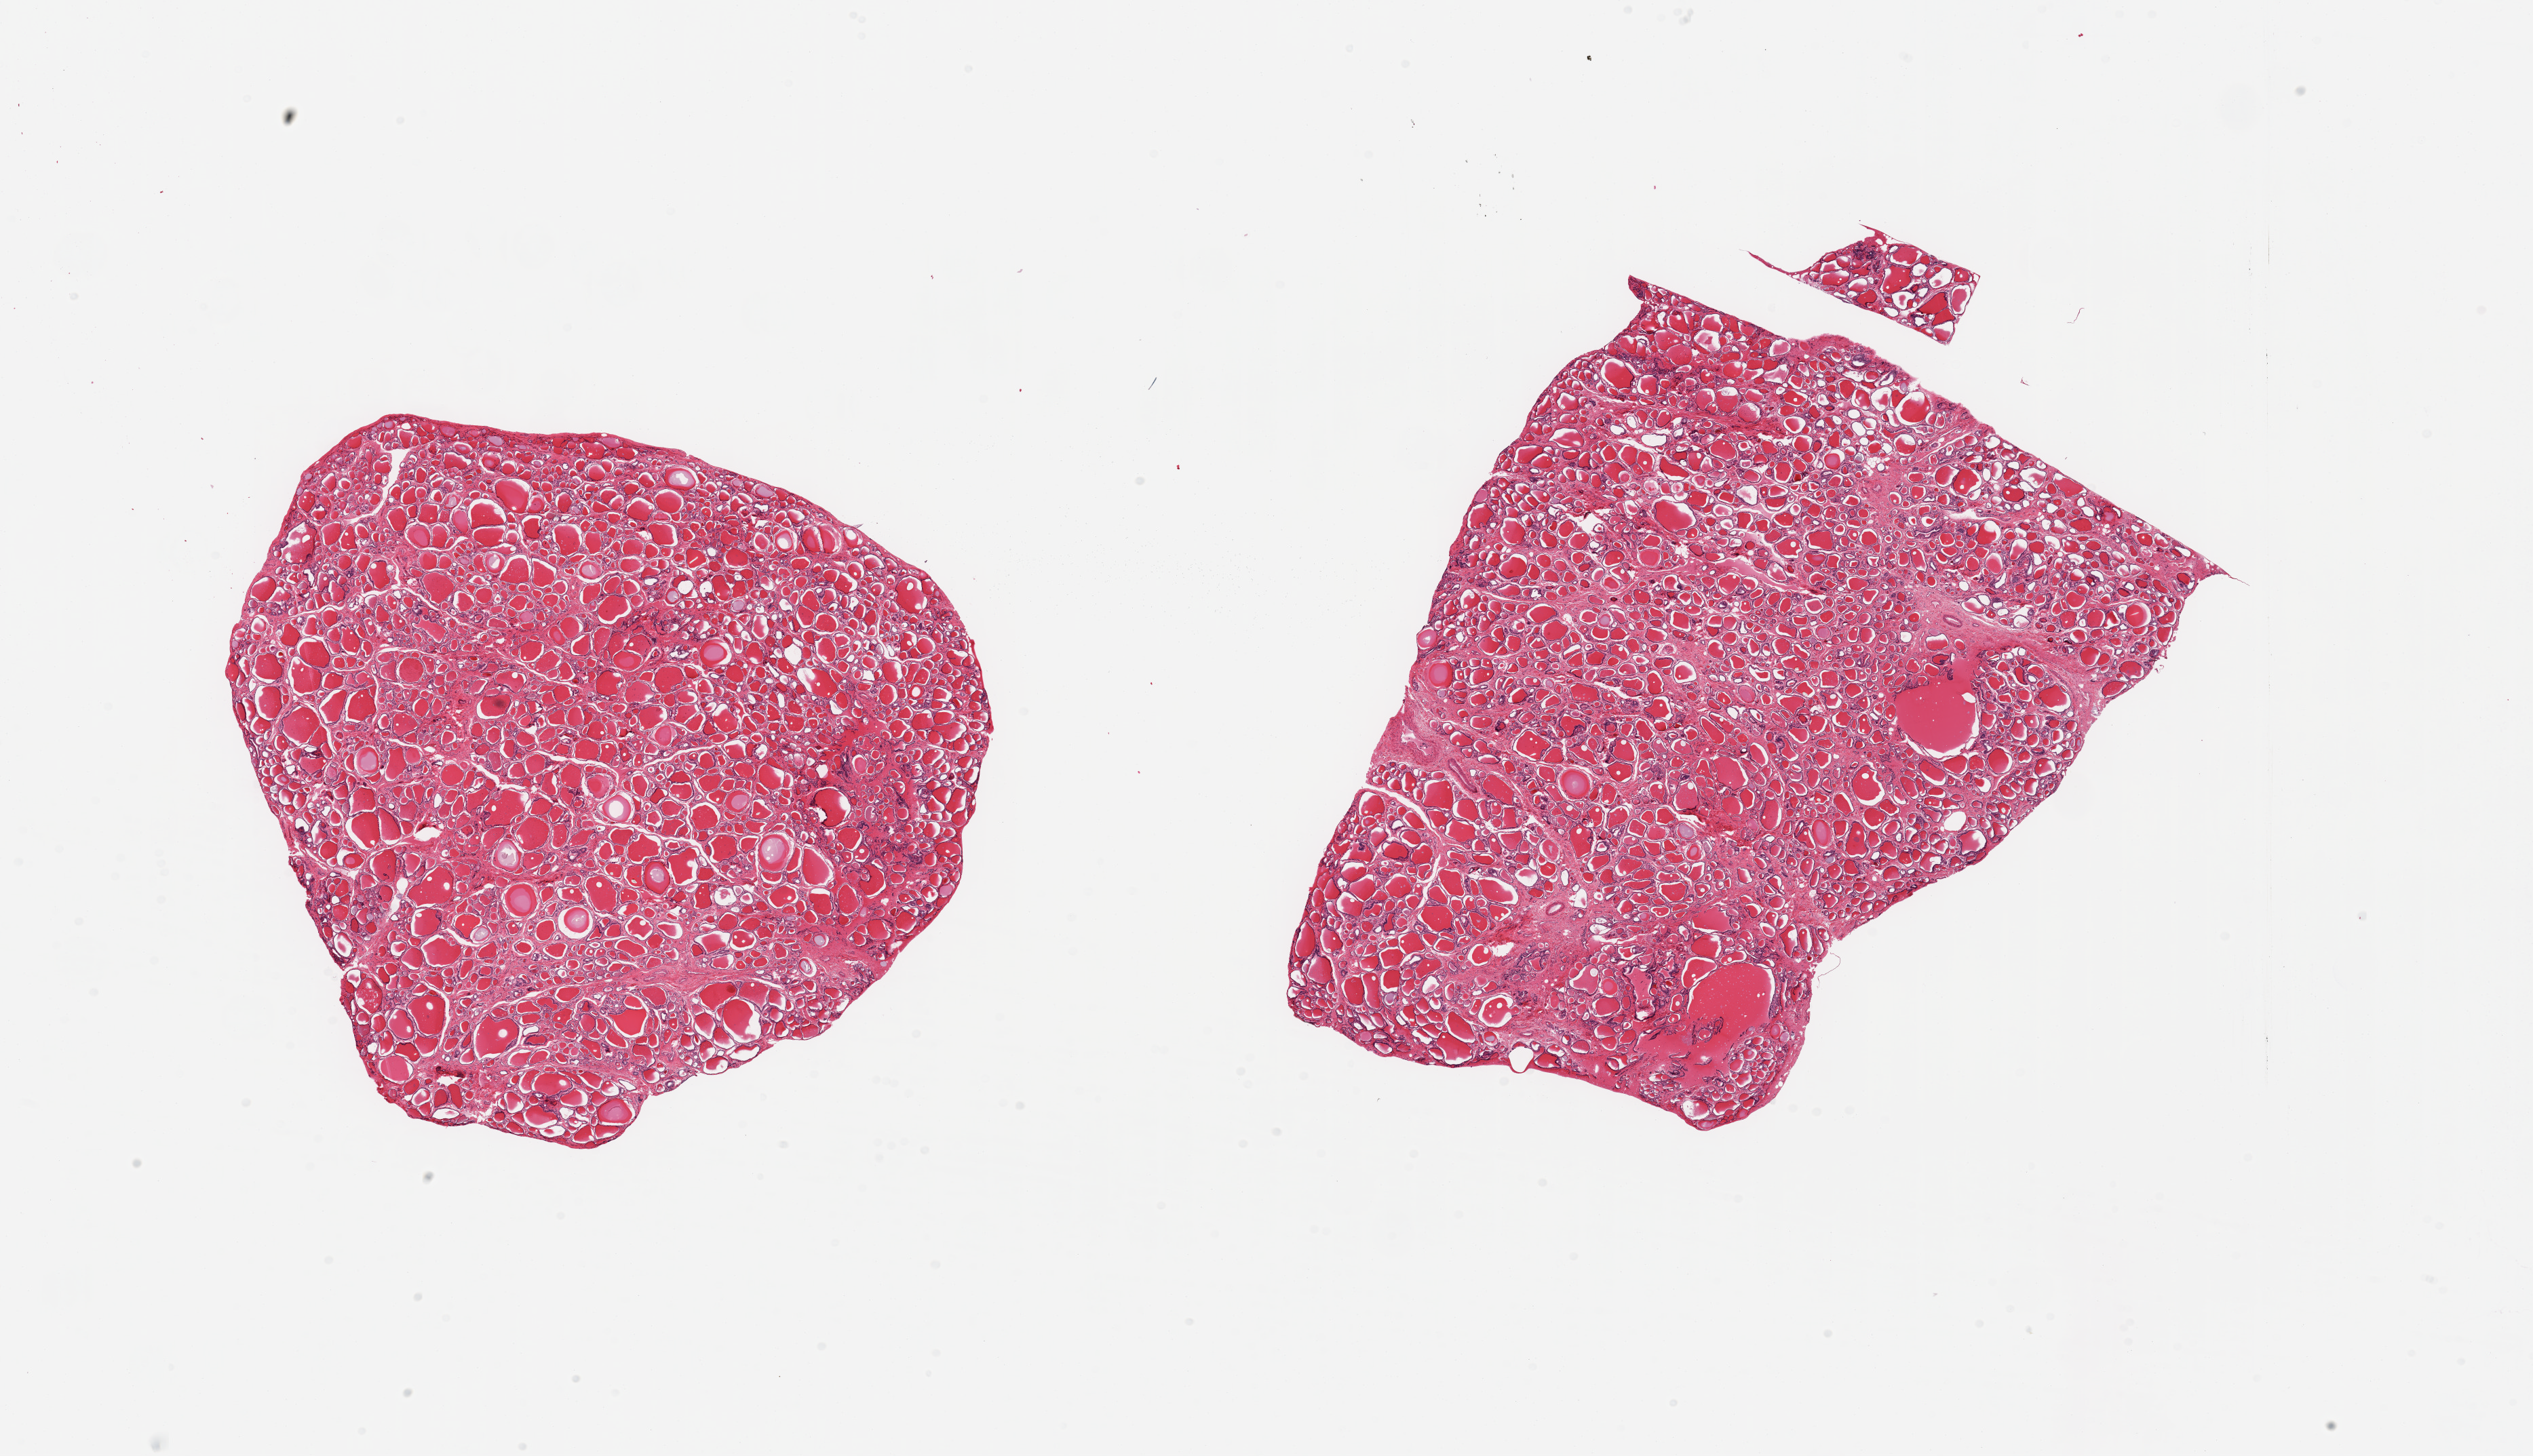
Digitized H&E-stained section, brightfield, shown as a low-resolution overview of the whole scanned area (about 29.5 x 17.0 mm, slide scanned at 20x); PAXgene-fixed paraffin-embedded (PFPE) section; section of thyroid (target tissue); donor tissue sample. Donor: female.
Reviewer comment on this tissue sample: 2 pieces; mild fibrosis.